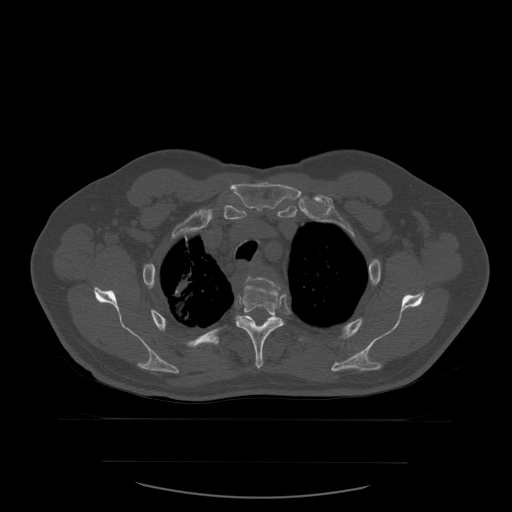
CT including the spine, one axial slice. Position 442 of 590 along the scan axis. Bone window (W 1800 / L 400 HU). 1.25 mm slice thickness. 512 × 512 image matrix, field of view 479 × 479 mm. Patient age 71 years. Case-level facts recorded for this patient, not image findings: primary cancer: lung.
Structures marked on this image (semi-automatically segmented with operator editing):
- T3 vertebra: bounding box [x1, y1, x2, y2] px = [247, 276, 281, 291]
- T4 vertebra: [235, 278, 284, 369]
- T5 vertebra: [221, 316, 256, 344]